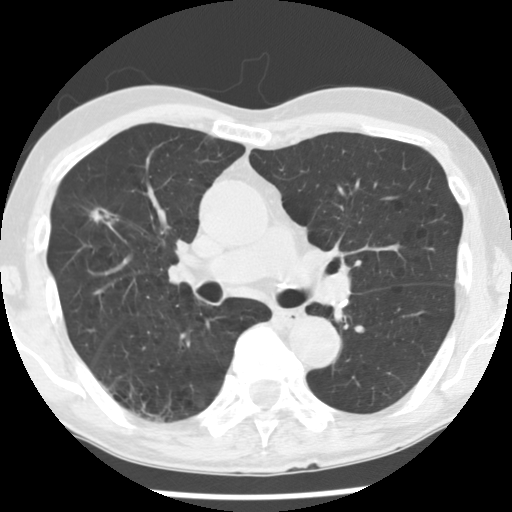
Chest CT (low-dose screening protocol), one axial image; baseline screening round; lung window (W 1500 / L -600 HU); slice 76 of 176 in the series. Male, age 72 years at enrolment.
Expert reader's lesion annotation, box from (x=76, y=193) to (x=130, y=243) px. Screening reader's record for this exam (one nodule recorded; not confirmed to be the boxed lesion): non-calcified nodule or mass ≥4 mm, right upper lobe, 11 × 8 mm, spiculated (stellate) margins, soft tissue attenuation. Later outcome: lung cancer diagnosed 72 days after this screen — bronchiolo-alveolar adenocarcinoma, NOS, right upper lobe, moderately differentiated (G2), stage IA (AJCC 6th edition), 10 mm at pathology.